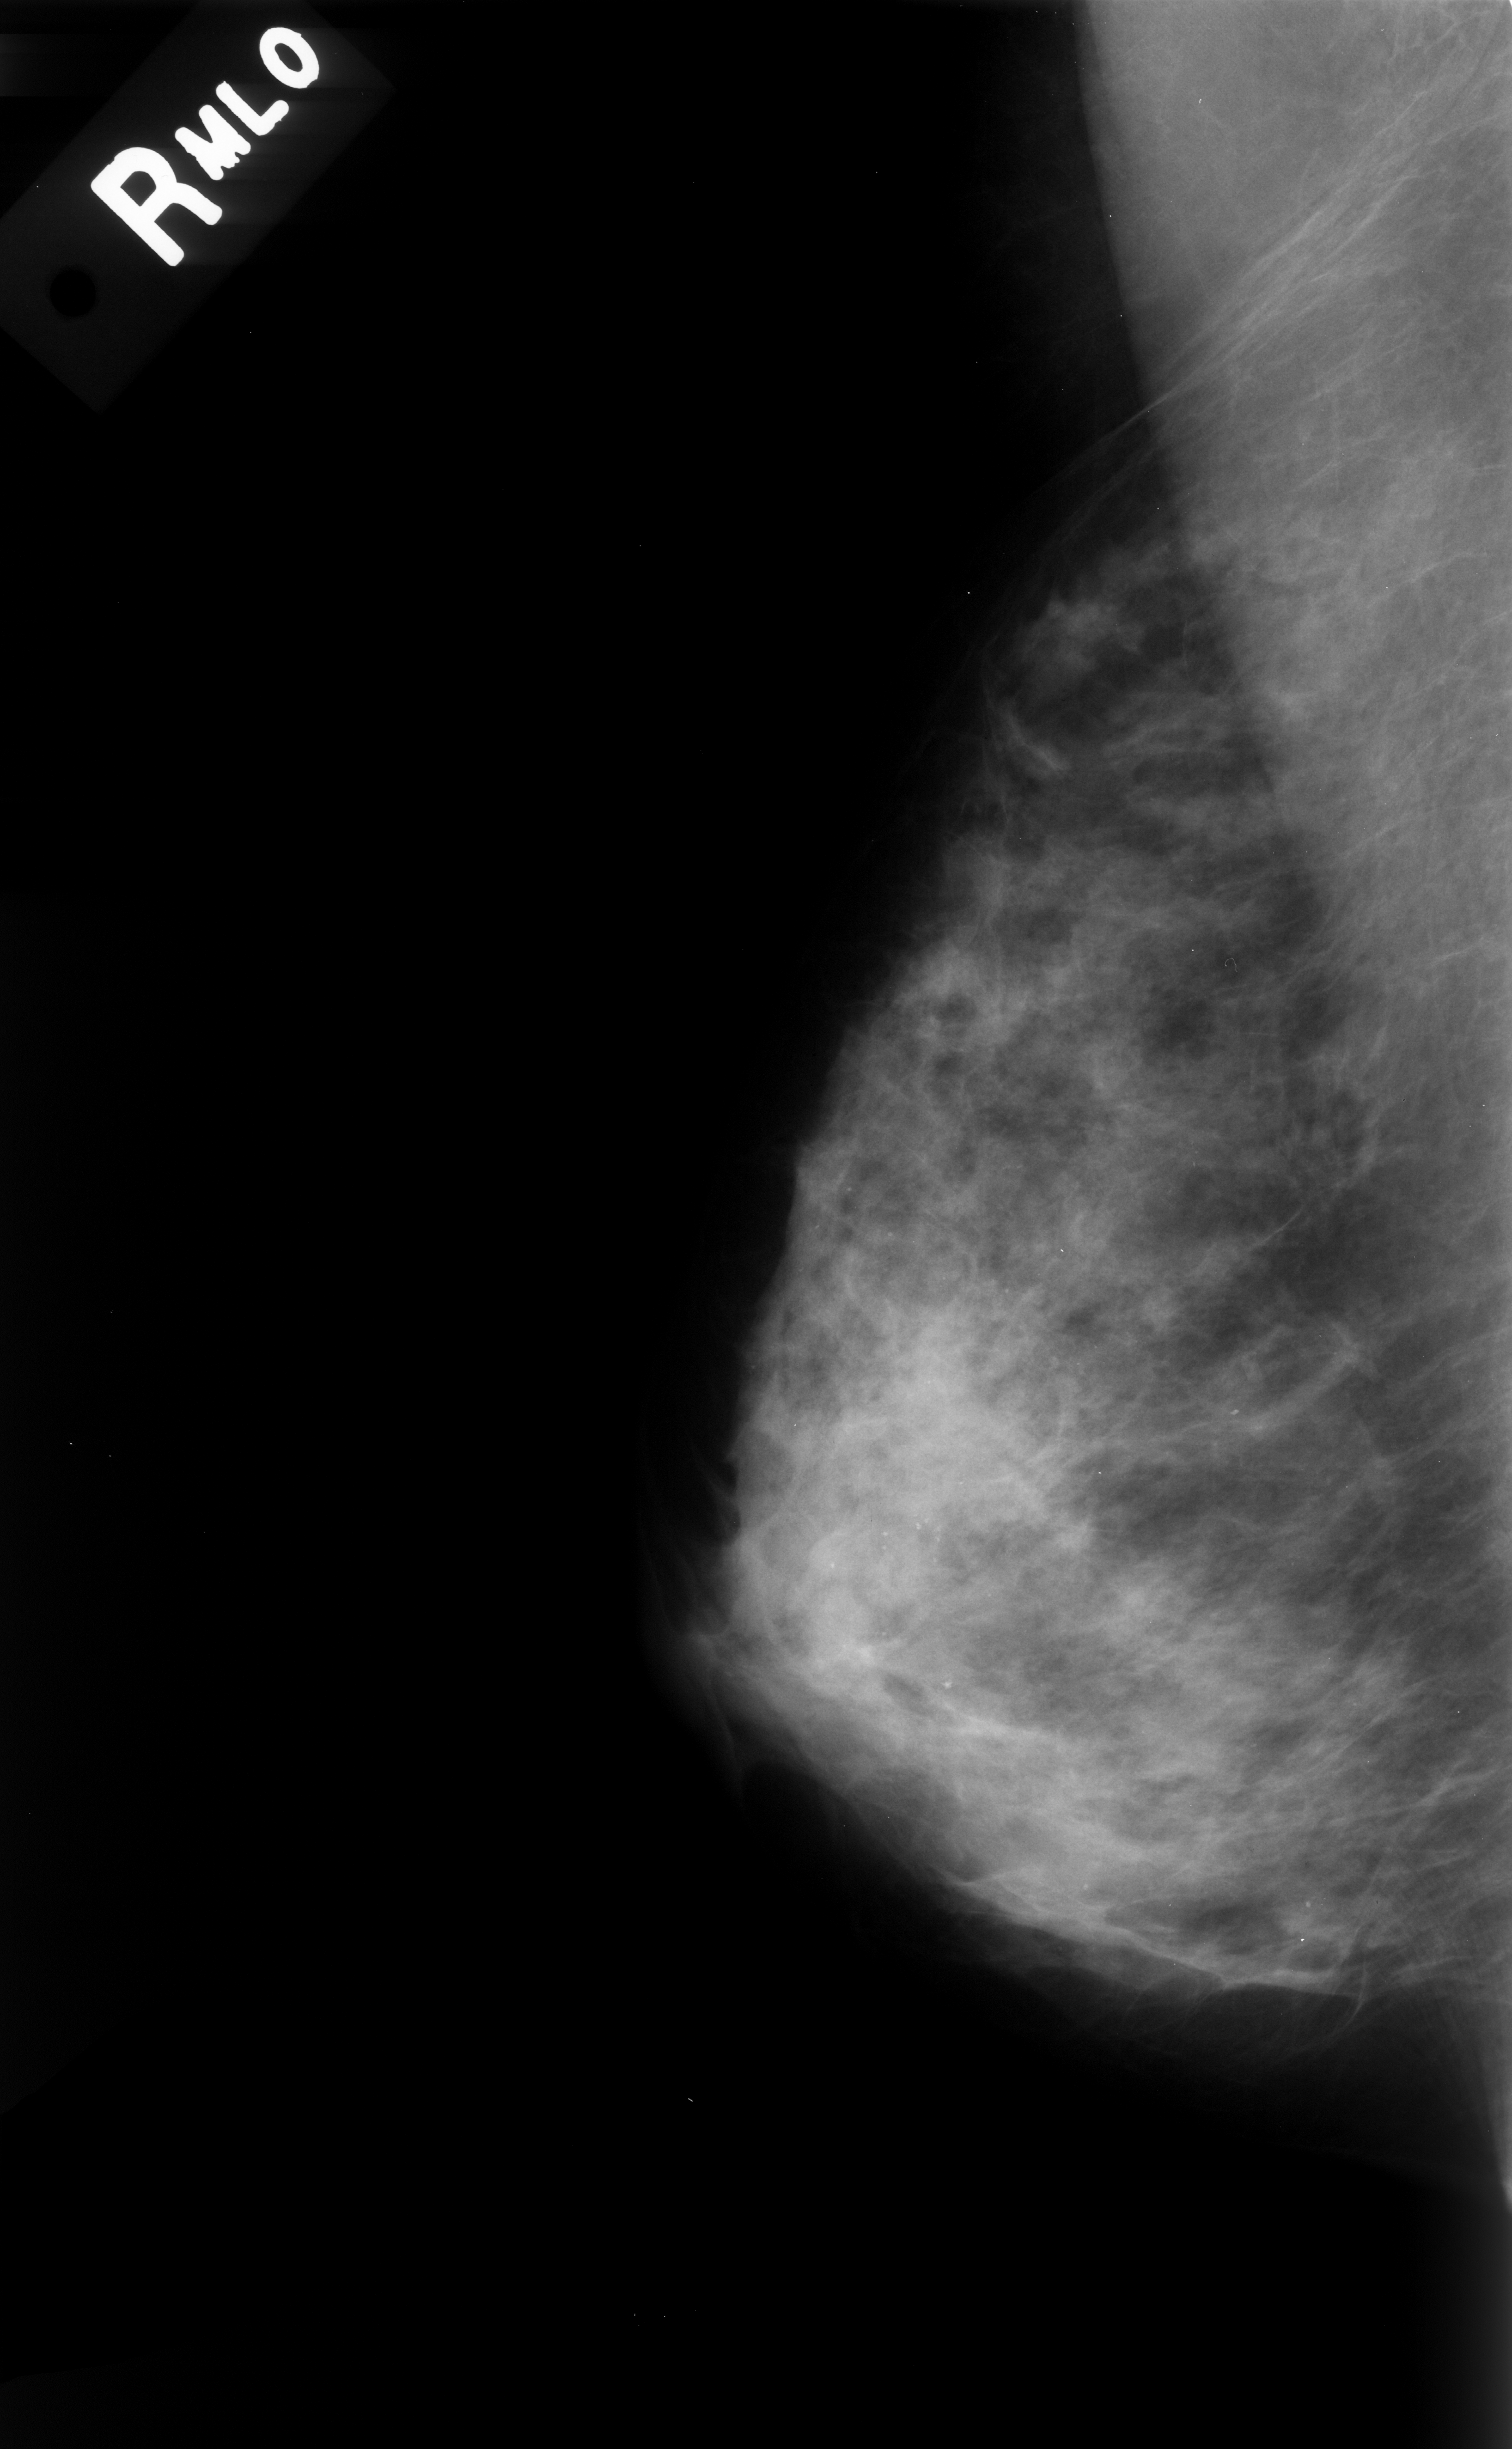
Mammogram (digitized film). Right breast. Mediolateral oblique (MLO) view. BI-RADS breast density category 3 (scale 1–4). 1512 × 2449 image matrix.
Marked abnormalities (boxes around the expert regions of interest):
- calcifications, morphology pleomorphic, distribution diffusely scattered; BI-RADS assessment category 3; subtlety rating 3 on a 1 (subtle) to 5 (obvious) scale; pathology result (as recorded, not read from the image): benign: bounding box <727,1028,1509,2019> (left, top, right, bottom; pixels)